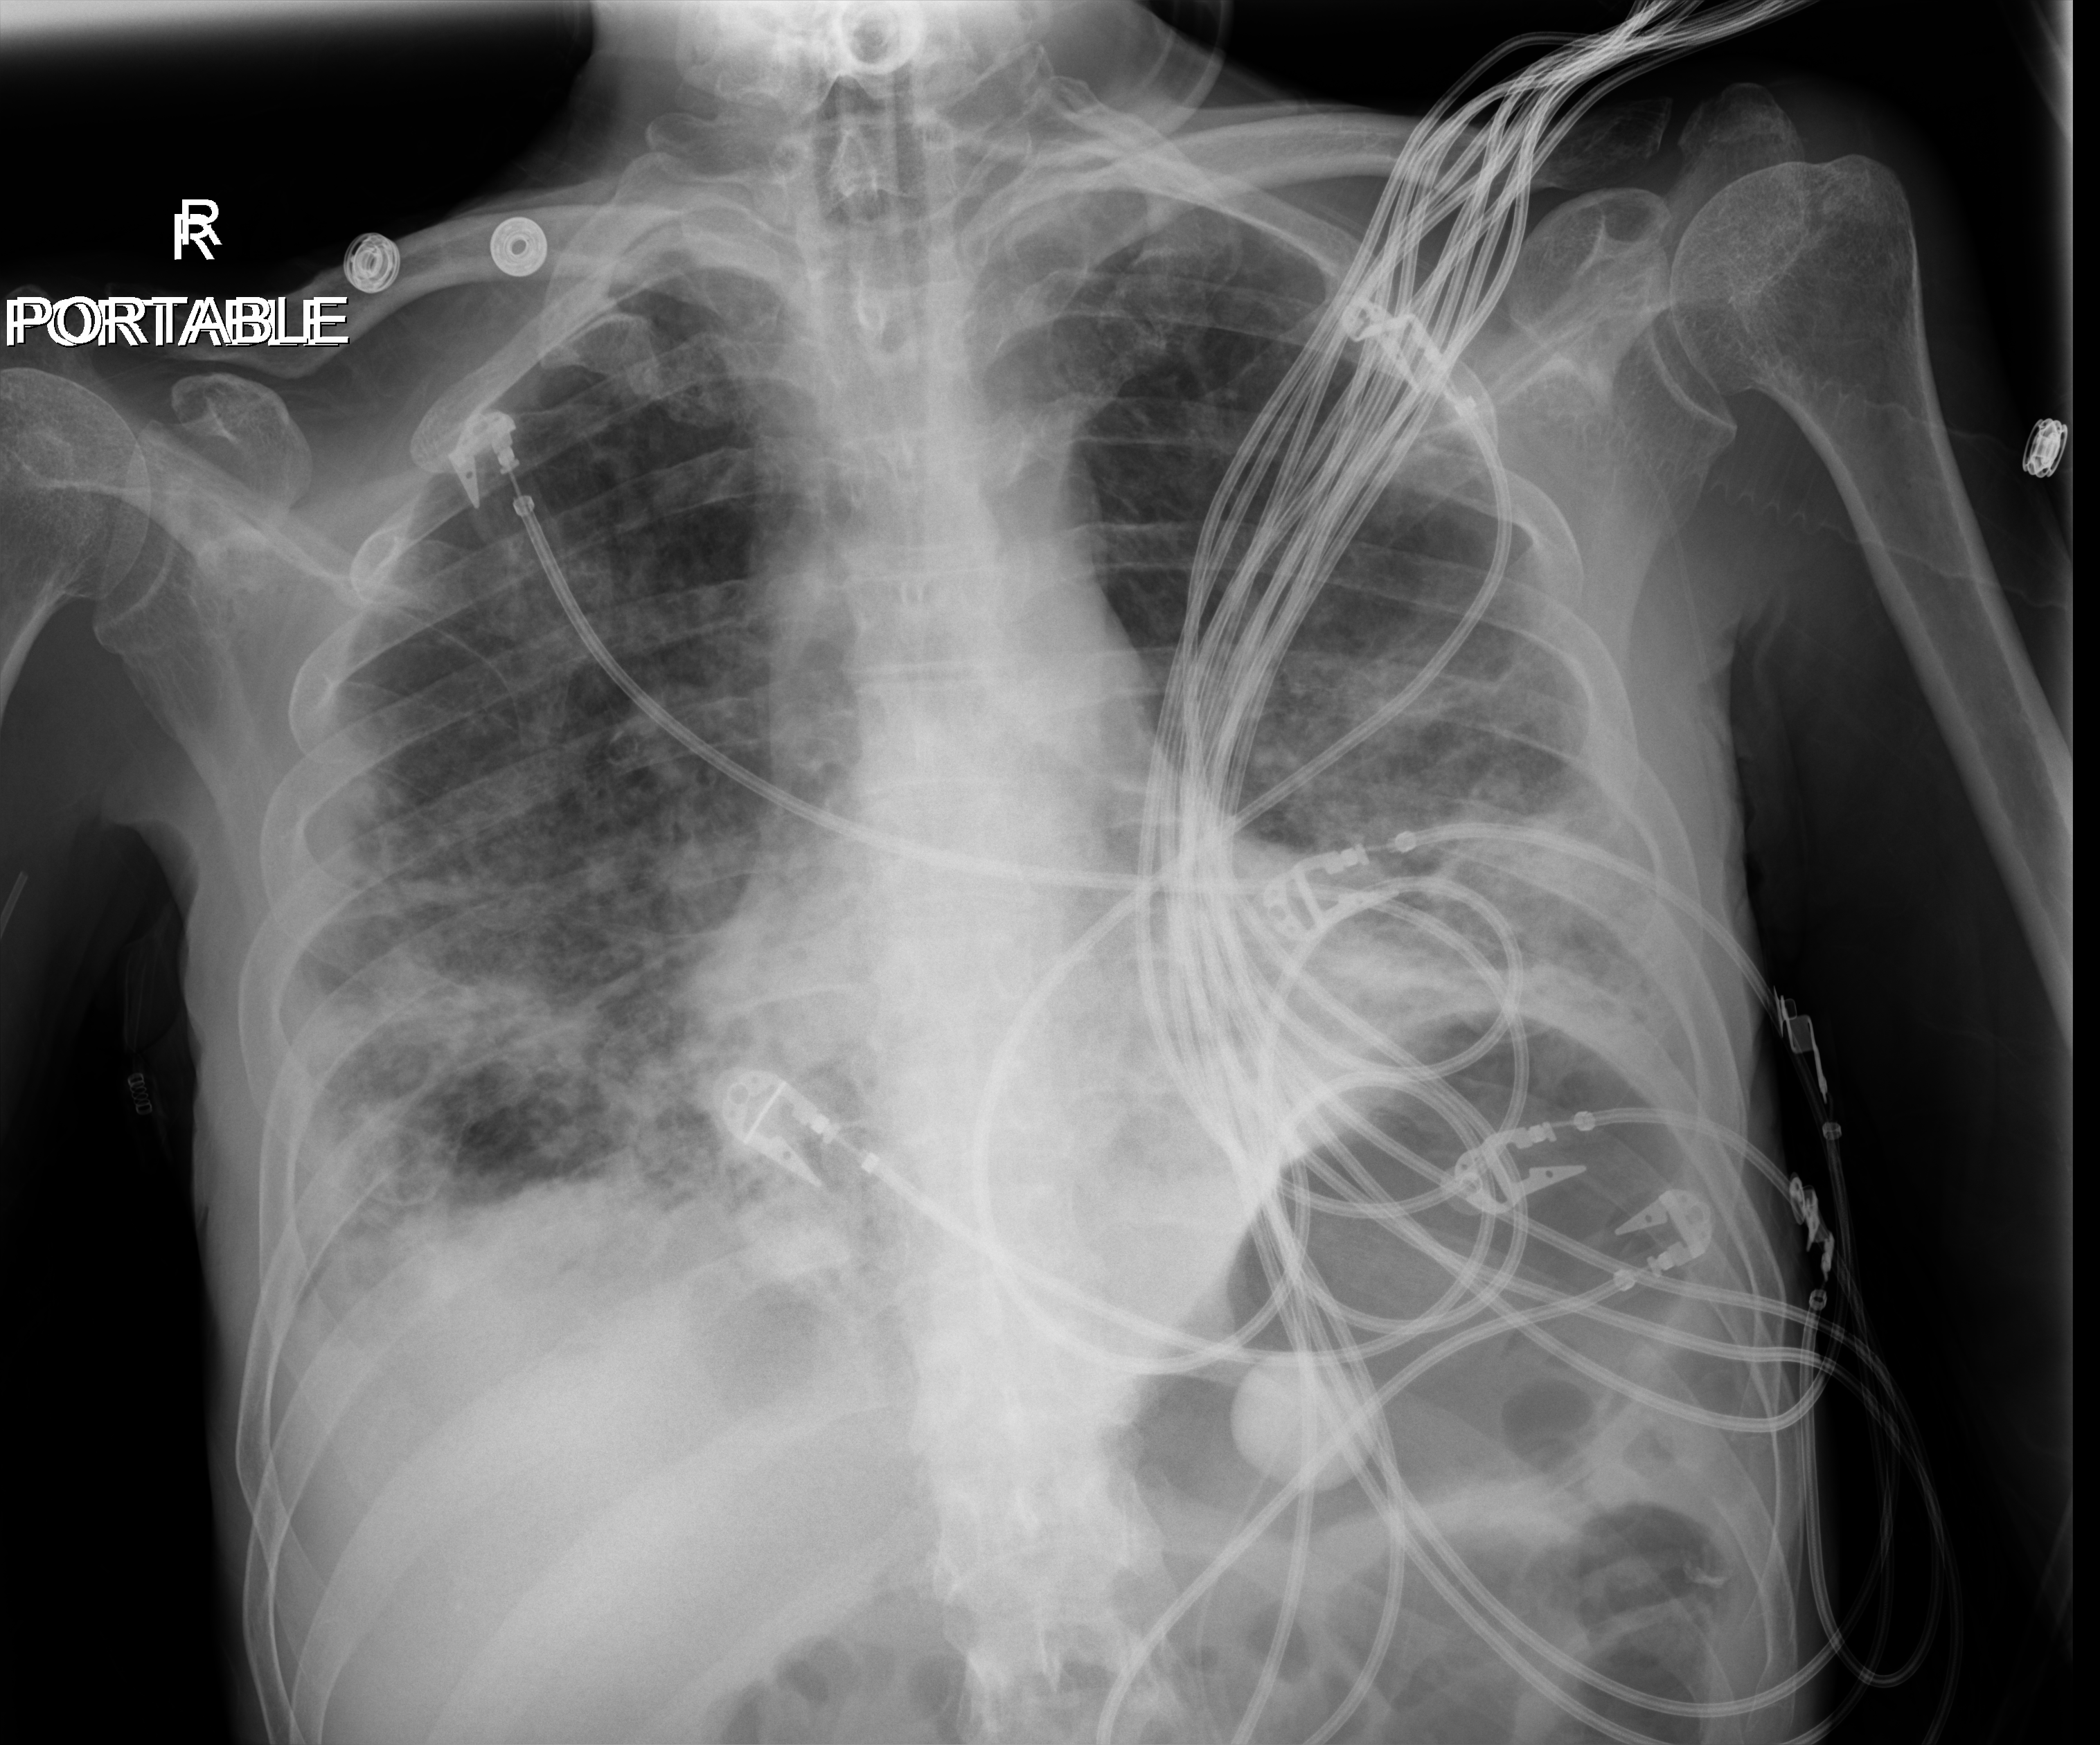
Chest X-ray, anteroposterior (AP) projection. Male patient hospitalised with COVID-19, age 18–59 years.
From the hospital-stay record, not from the radiograph (when in the stay this image was taken is not recorded):
- hypertension (admission record): yes
- length of hospital stay: 96 days